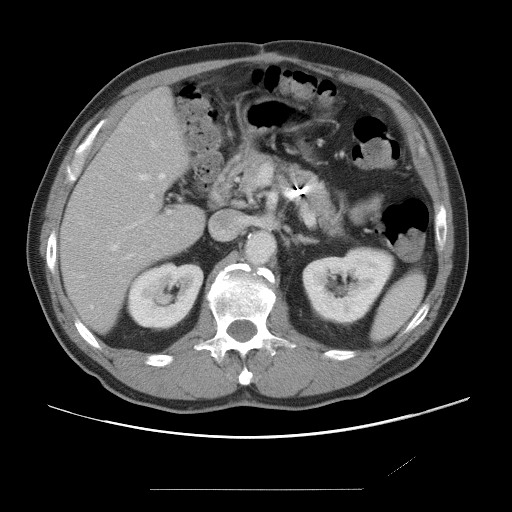
Contrast-enhanced abdominal CT, one axial slice. 120 kVp. Intravenous contrast given. Soft-tissue window (W 400 / L 40 HU). 512 × 512 image matrix. Male patient, age 74 years. From the clinical record (not read from this slice): diagnosis: colorectal cancer liver metastases, imaged before liver resection; multiple liver metastases: yes; largest metastasis: 1.1 cm; disease in both lobes: no.
Annotated regions visible in this slice (expert manual segmentation):
- hepatic veins: bounding box (x1, y1, x2, y2) in pixels: (90, 143, 165, 308)
- liver: (63, 89, 205, 329)
- planned liver remnant (the part of the liver to remain after resection): (63, 89, 205, 329)
- portal vein (with intrahepatic branches): (150, 165, 273, 226)